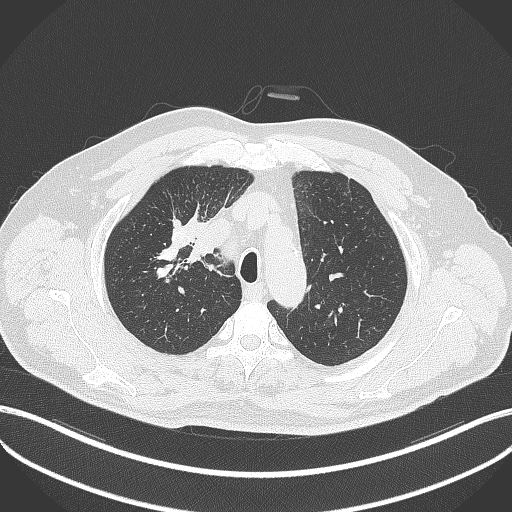
Chest CT, one axial slice. Position 307 of 411 along the scan axis. Reconstruction kernel B70f. Lung window (W 1500 / L -600 HU). 1 mm slice thickness. 512 × 512 image matrix. Patient: male, 60 years. From the clinical record (not read from this slice): clinical TNM (as recorded): T1b N1 M0.
Structures marked on this image (rectangle marked by the reading radiologist):
- lung tumour (recorded histology: squamous cell carcinoma): bounding box <182,239,213,262> (left, top, right, bottom; pixels)